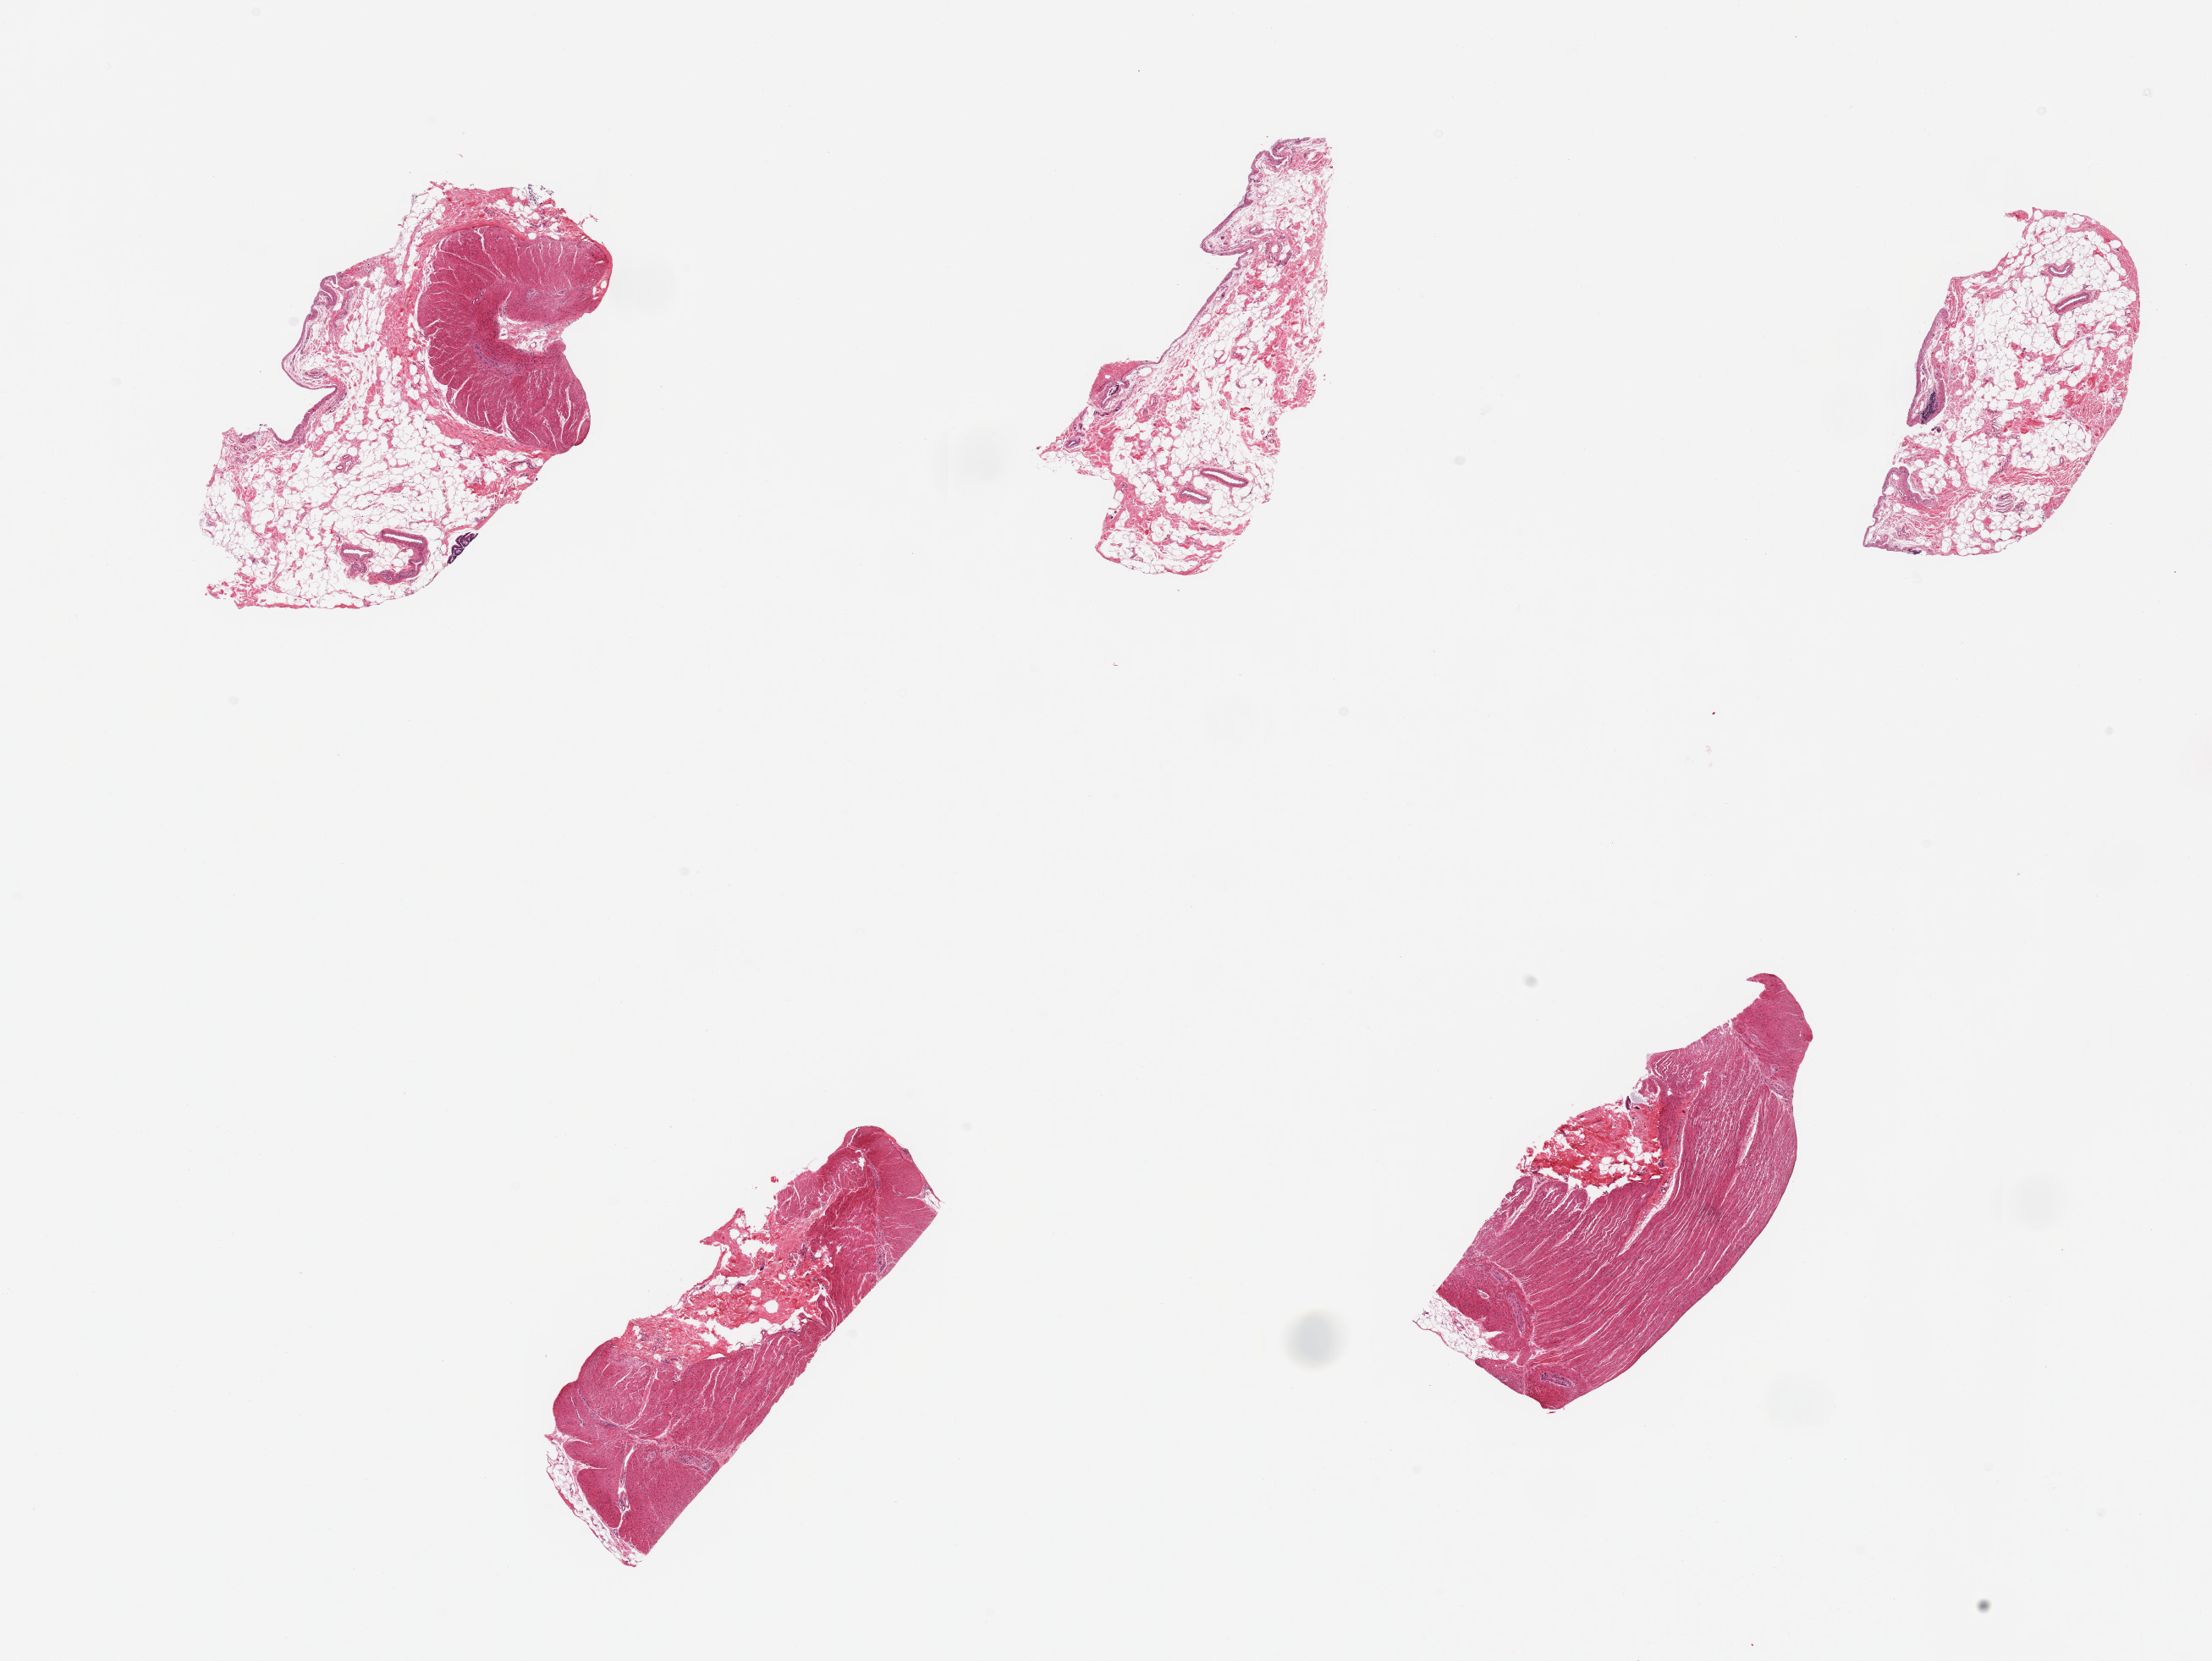
Digitized hematoxylin and eosin (H&E)-stained section, brightfield — low-resolution overview of the scanned area, about 20.7 x 15.5 mm (slide scanned at 20x); PAXgene-fixed paraffin-embedded (PFPE) section; sampled site (target tissue): transverse colon; donor tissue sample. Male donor.
• reviewer comment on this tissue sample: 6 pieces fat/muscularis, no target mucosa